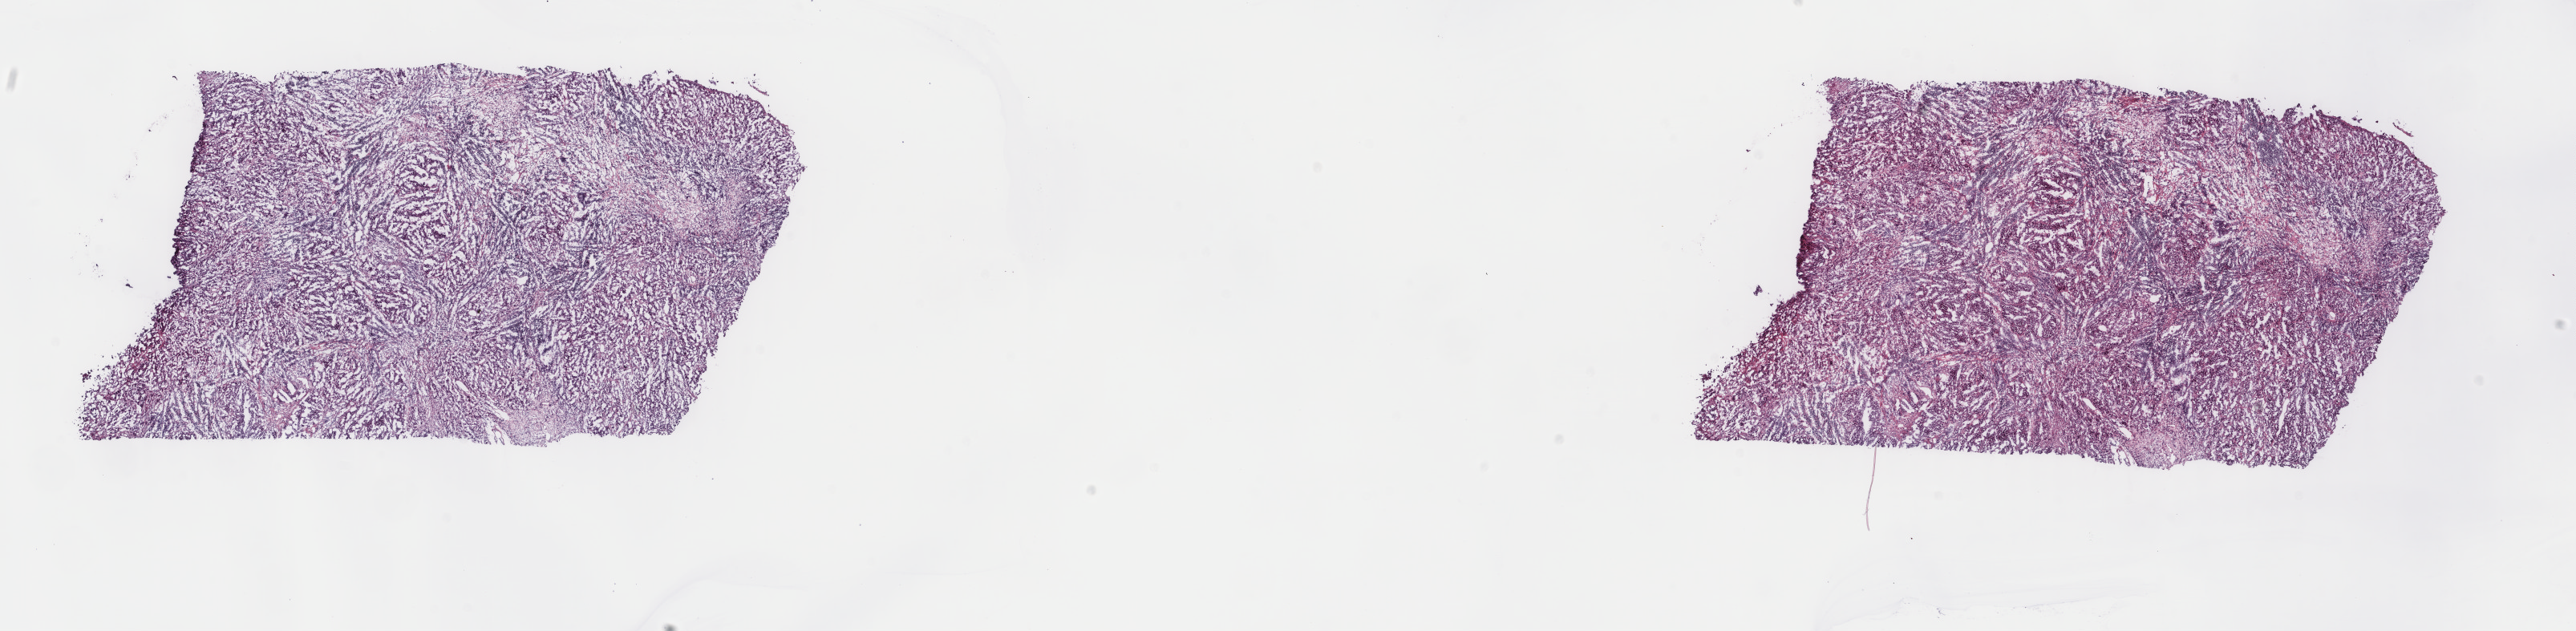
H&E-stained whole-slide image — a low-resolution overview of the entire scanned area, about 25.5 x 6.2 mm (slide scanned at 40x). Frozen section. Metastatic tumour sample. Female patient; age at initial diagnosis 56 years. Pathologist review of this section (percent, as recorded): tumour cells 100%, tumour nuclei 80%.
This section: metastatic tumour tissue. Patient diagnosis: Malignant melanoma, NOS.